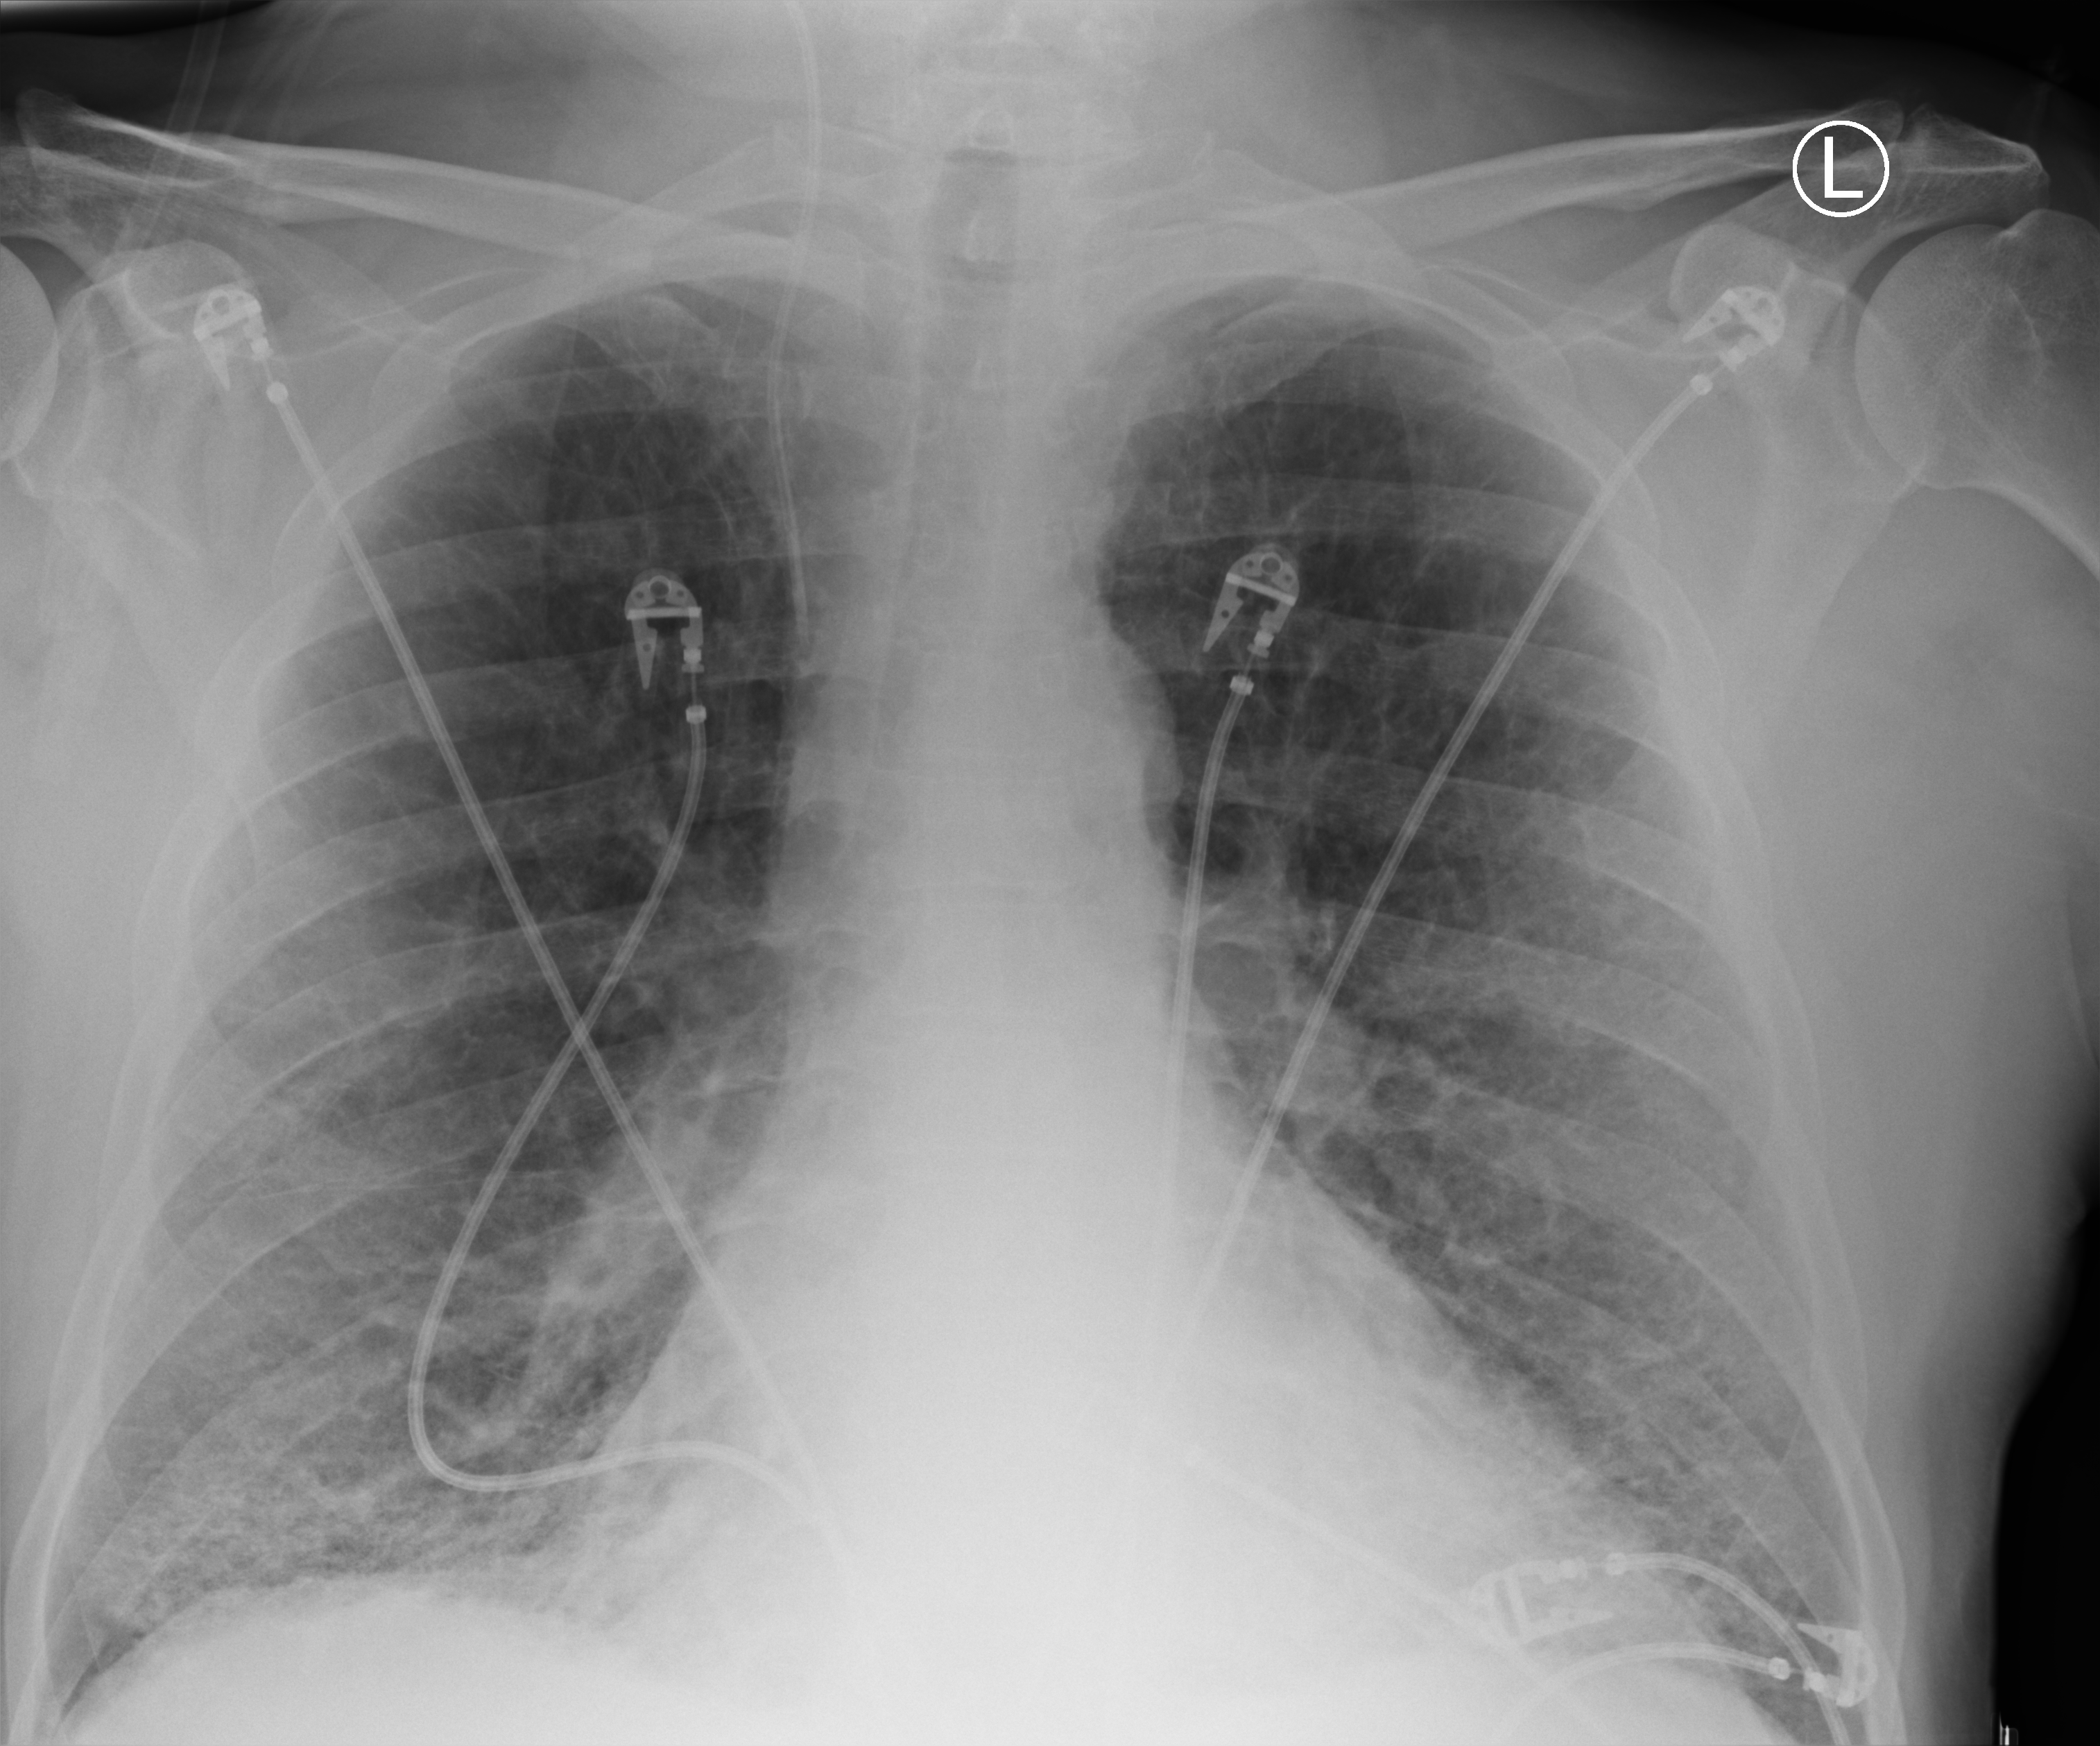
Portable chest radiograph, anteroposterior (AP) projection. Patient hospitalised with COVID-19, aged 18–59 years.
Admission-level facts for this patient (not findings on this image; timing relative to this image not recorded): mechanically ventilated during this hospital stay: no; COPD (admission record): yes; smoking status (admission record): former.